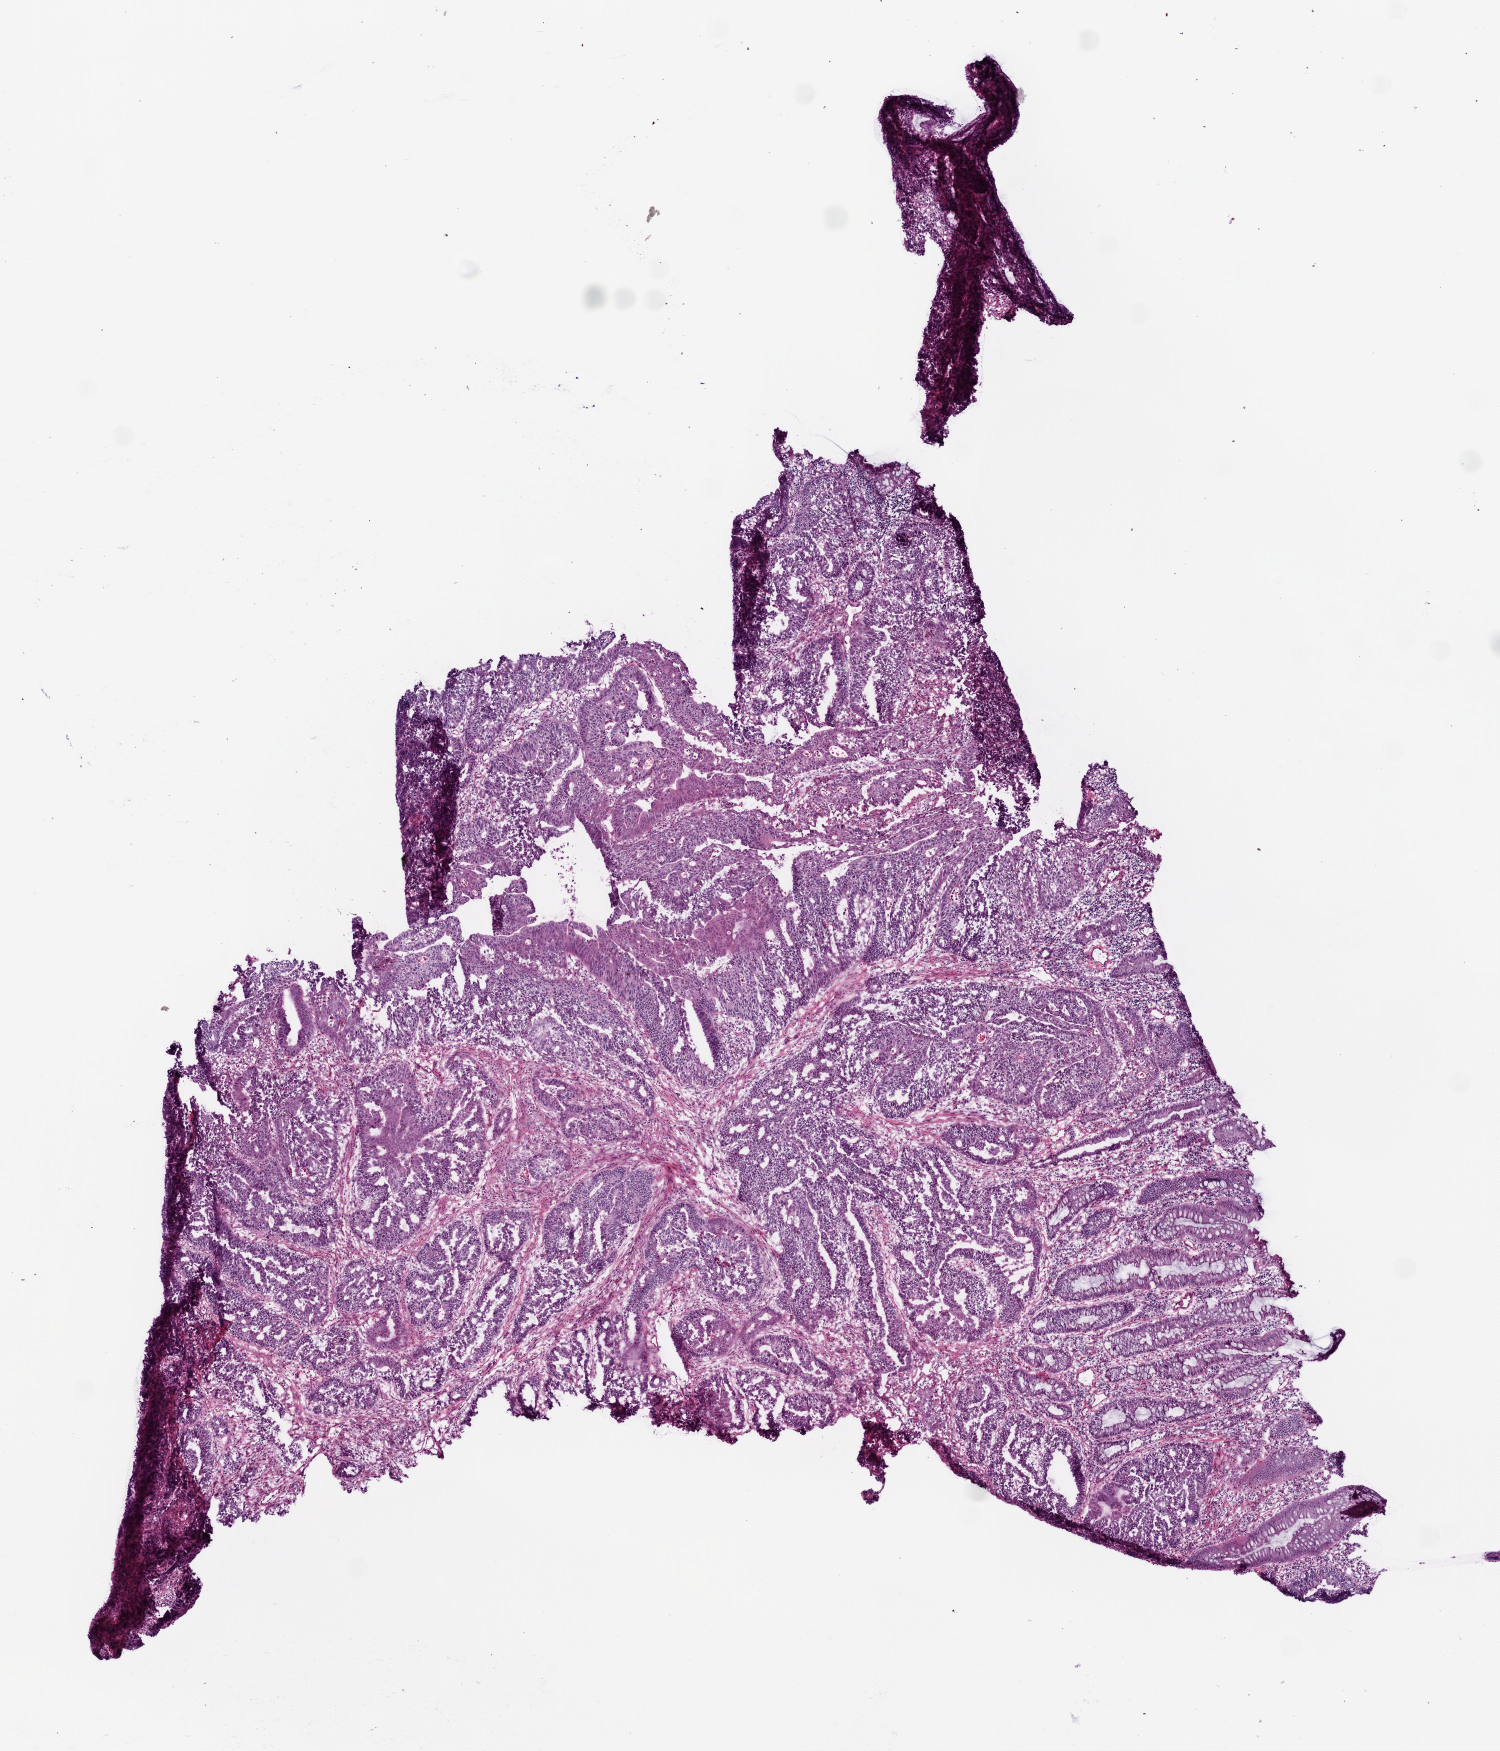
Digitized H&E-stained tissue section (whole slide) — shown as a low-resolution overview of the whole scanned area (about 6.0 x 7.0 mm, slide scanned at 20x), frozen section, colon, primary tumour sample. Patient: female, age at initial diagnosis 51 years. Slide review estimates, as recorded: tumour cells 80%, tumour nuclei 90%, normal cells 0%, stromal cells 20%, necrosis 0%.
TNM: T3 N0 M0. Diagnosis: Adenocarcinoma, NOS. Lymph nodes positive (case pathology): 0 of 33 examined. AJCC pathologic stage: II (5th edition).